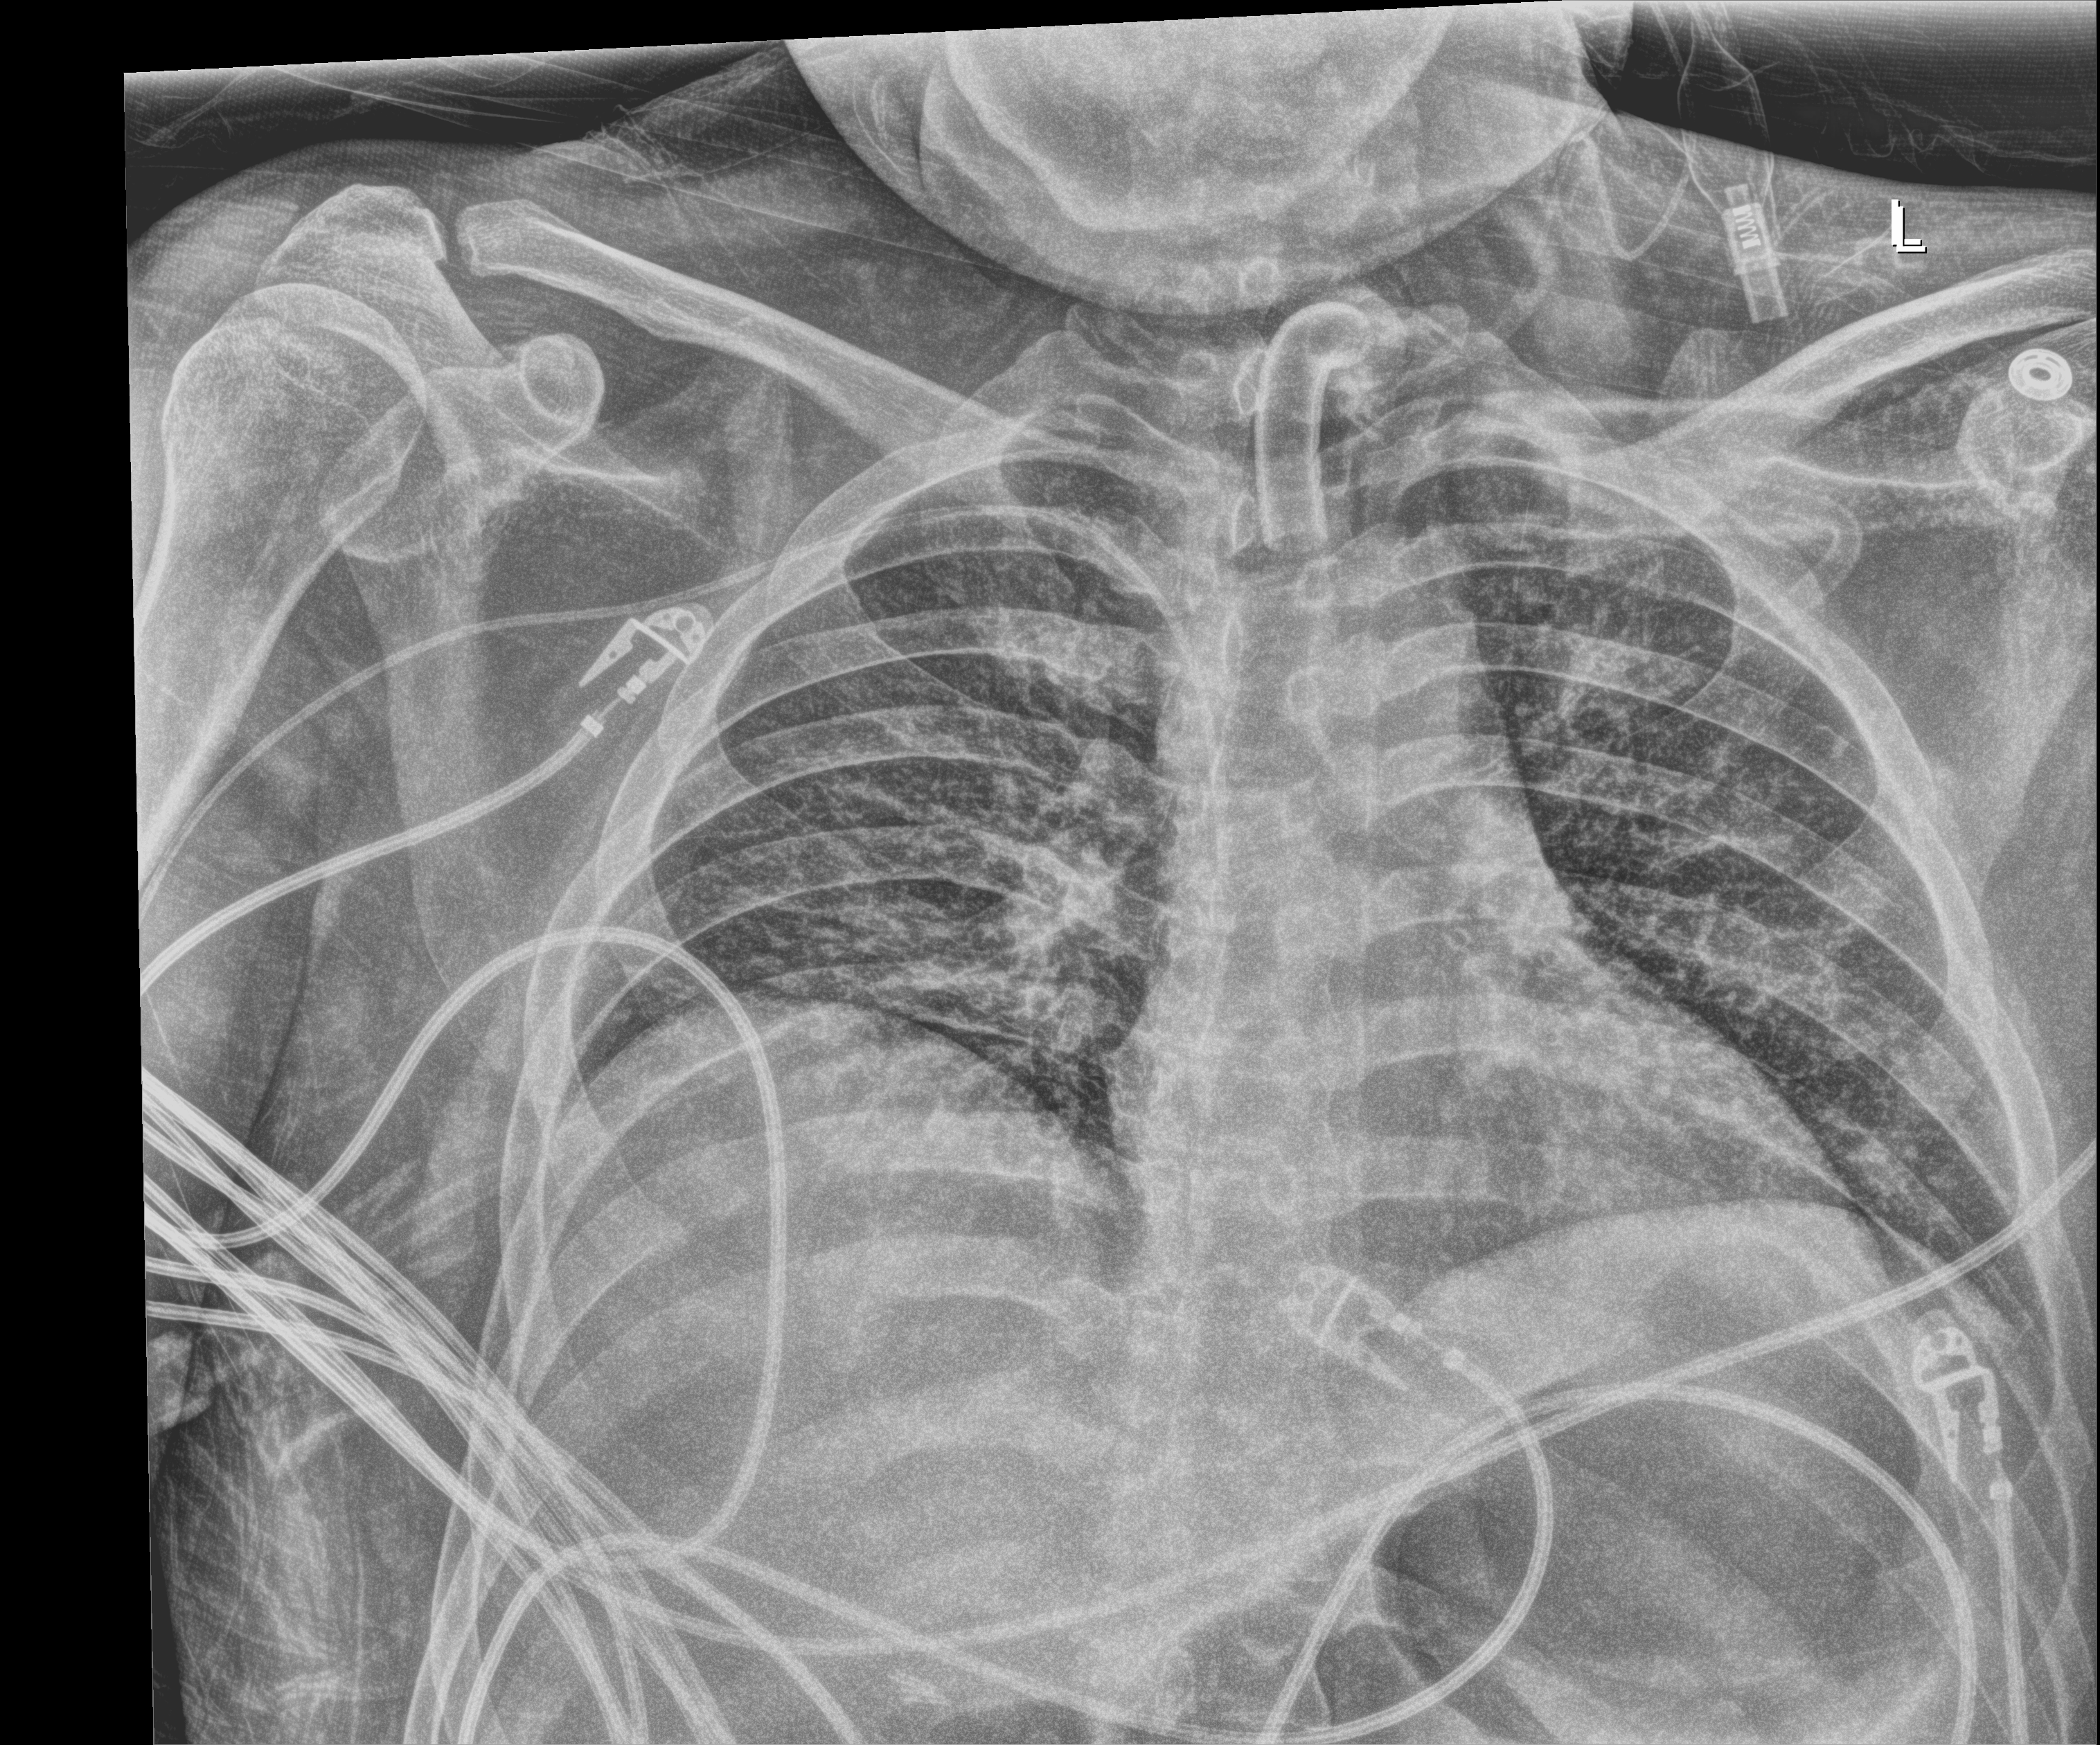
Chest X-ray (portable). Male patient hospitalised with COVID-19, age 18–59 years.
Hospital-stay facts (about this admission, not read from this image; timing relative to this image not recorded):
- smoking status (admission record): former
- COPD (admission record): no